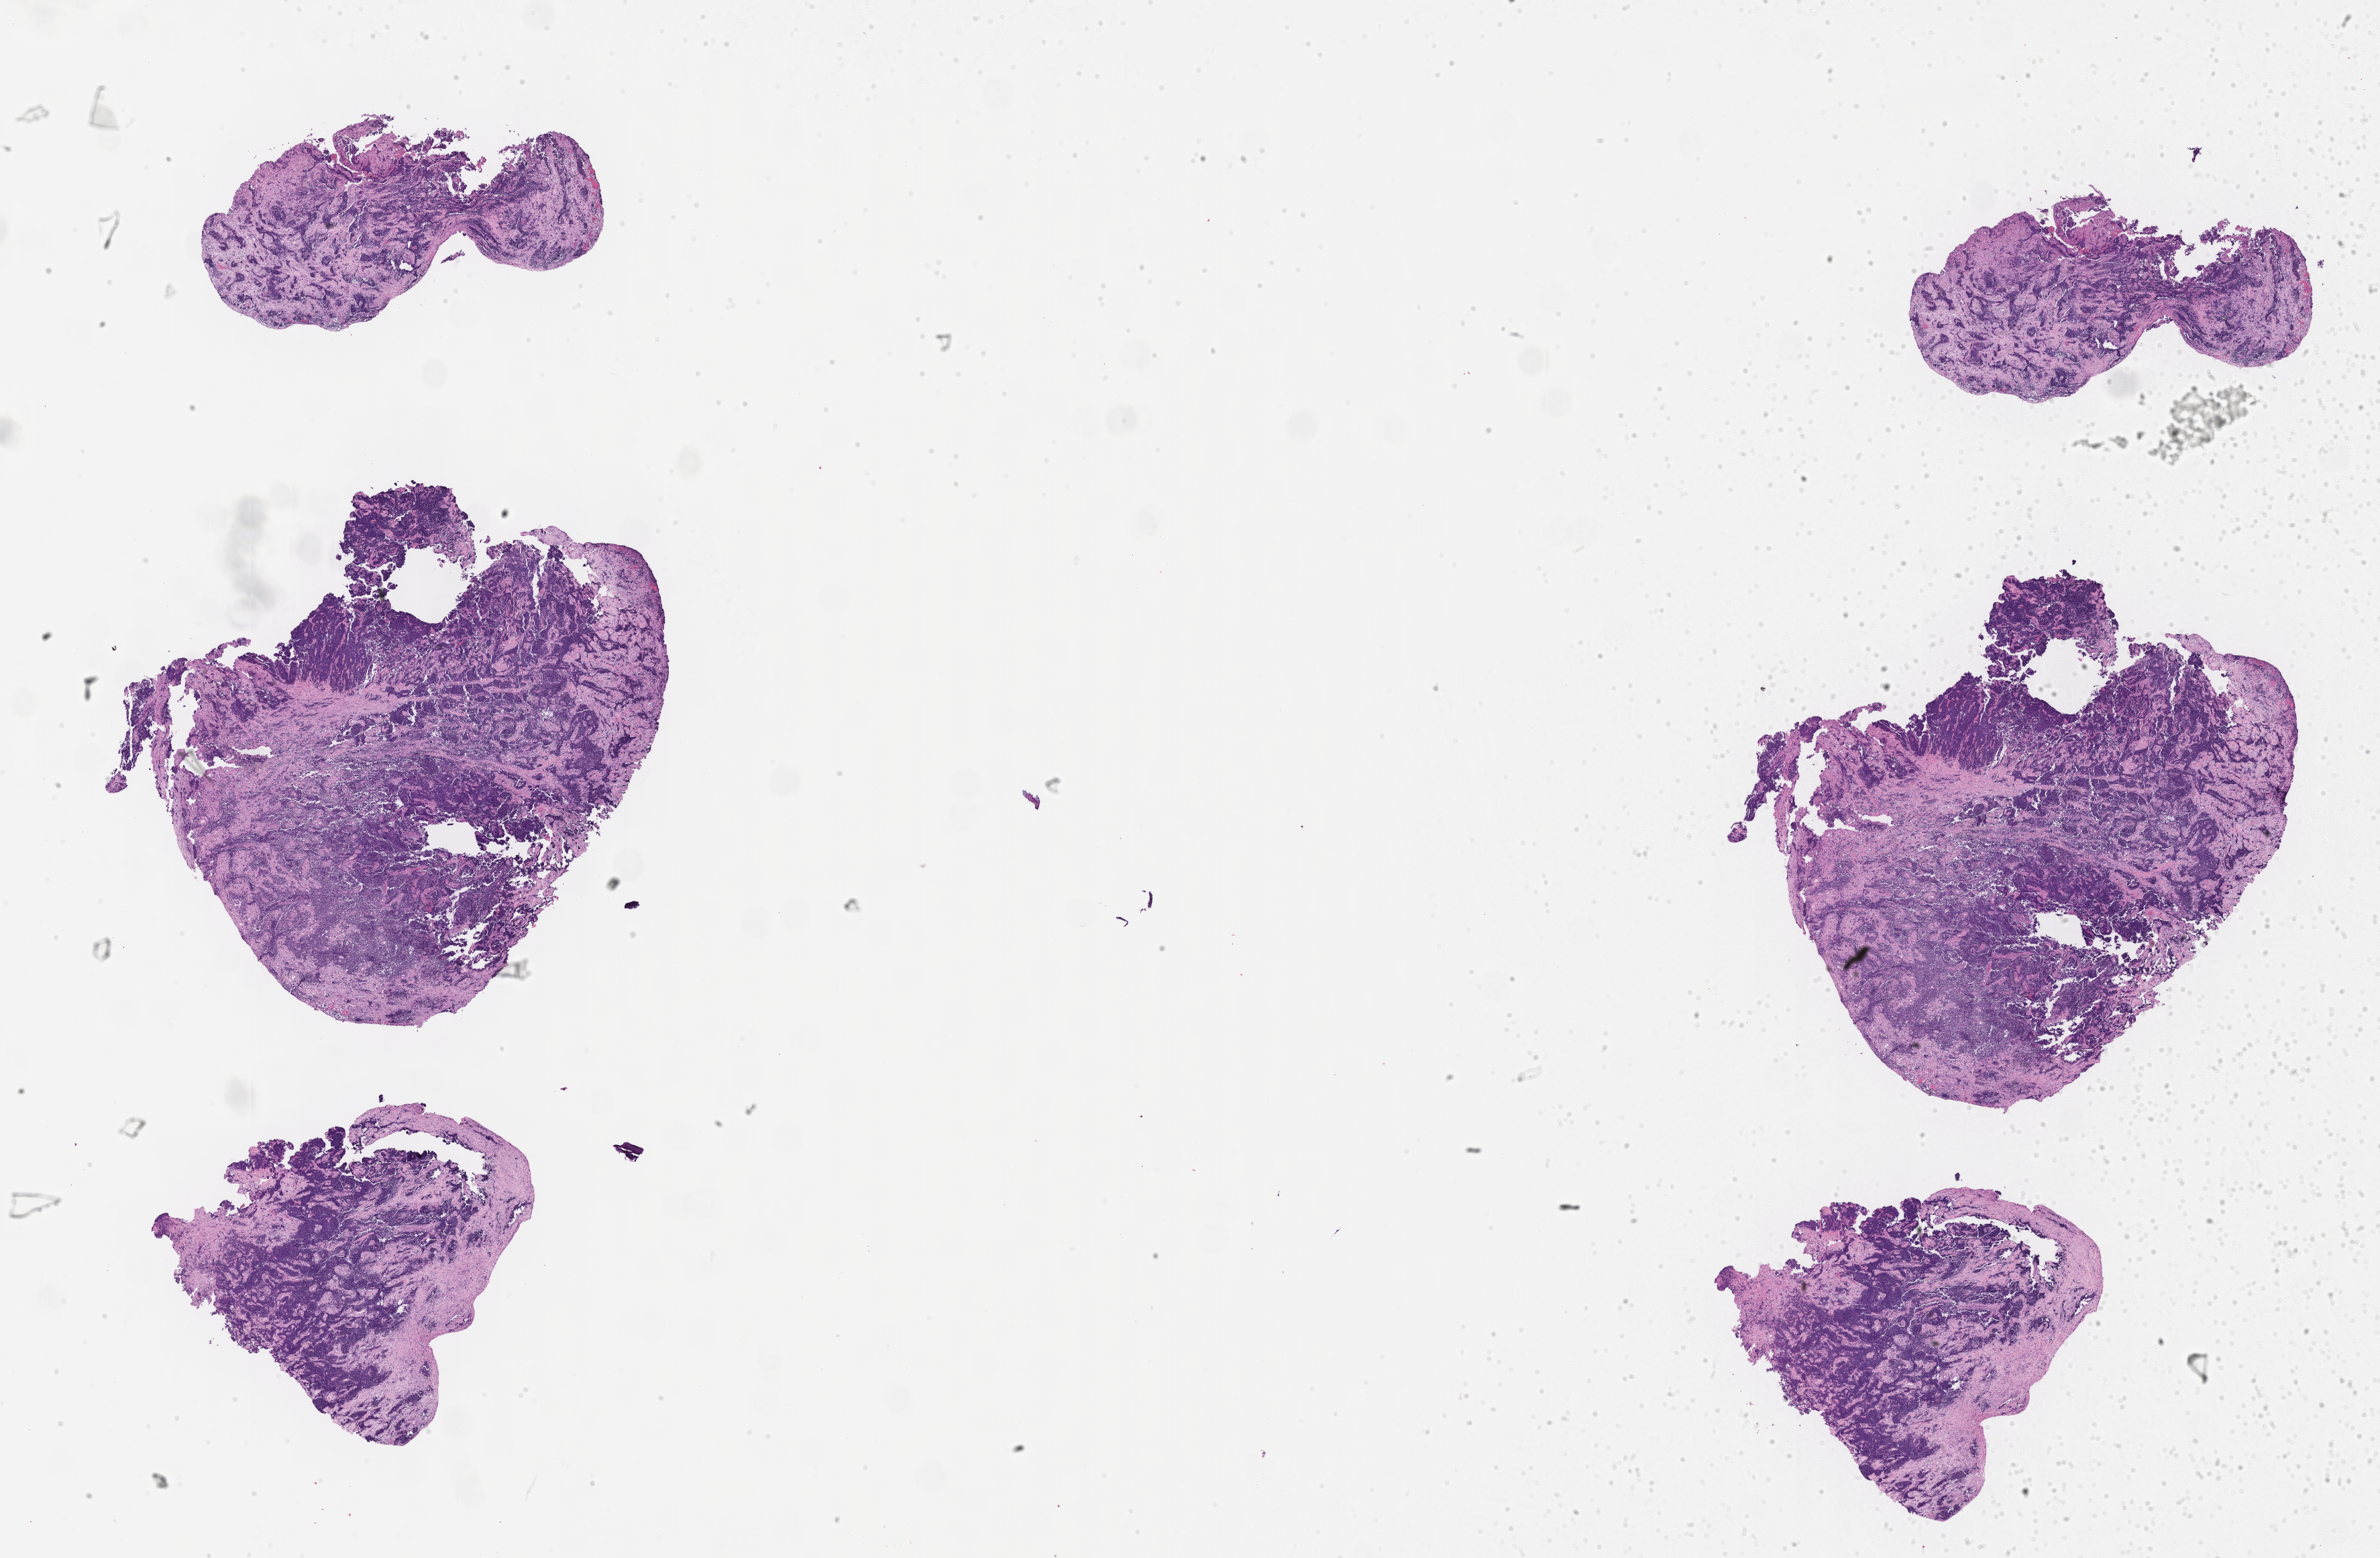
Whole-slide image, haematoxylin and eosin stain of tumor tissue, shown as a low-resolution overview of the whole scanned area (about 28.7 x 18.8 mm), FFPE section, sample anatomic site: abdomen. Female patient, age at diagnosis 3.3 years.
* metastatic status at presentation (as recorded): metastatic (confirmed)
* diagnosis: rhabdomyosarcoma; histological classification: alveolar rhabdomyosarcoma
* stage (as recorded): 4